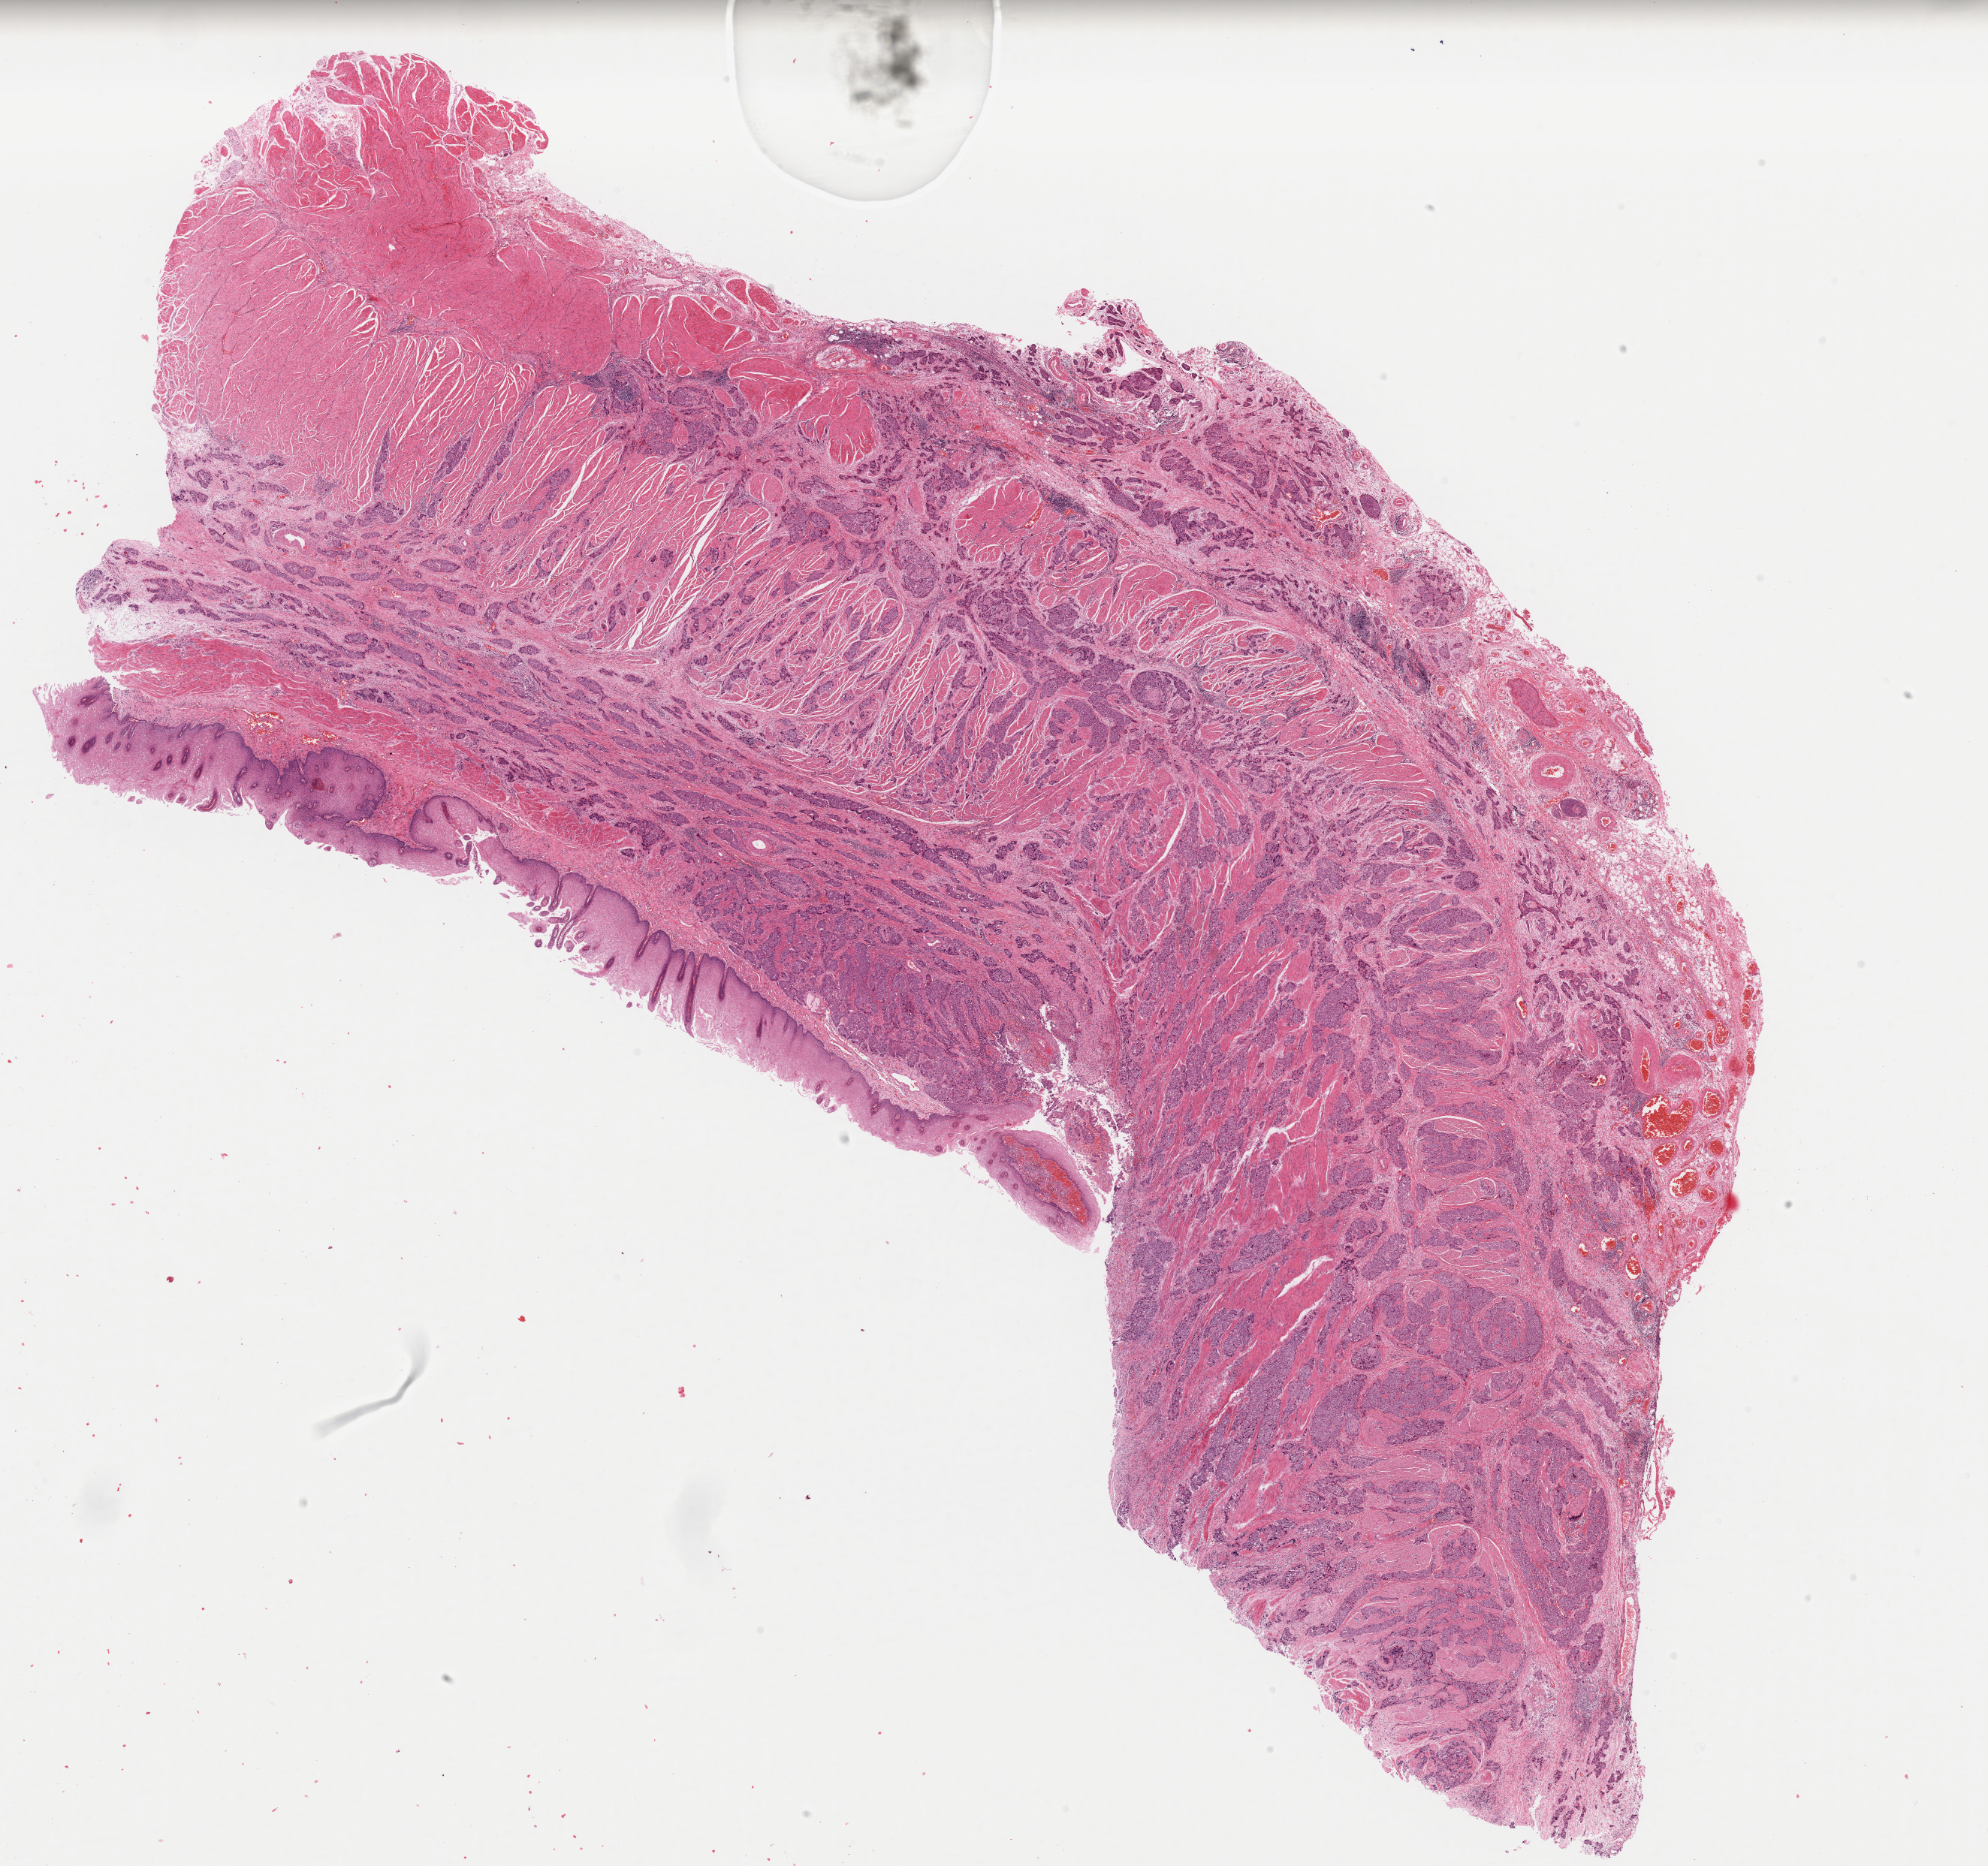
H&E-stained whole-slide image — low-resolution overview of the scanned area, about 20.9 x 19.6 mm (slide scanned at 40x). Formalin-fixed paraffin-embedded (FFPE) diagnostic section. Sample: primary tumour, esophagus. Patient: male, age at initial diagnosis 60 years. Histologic grade: G2 (moderately differentiated).
AJCC pathologic stage: IIIB (7th edition). TNM: T3 N2 M0. Pathologic diagnosis: Squamous cell carcinoma, NOS.